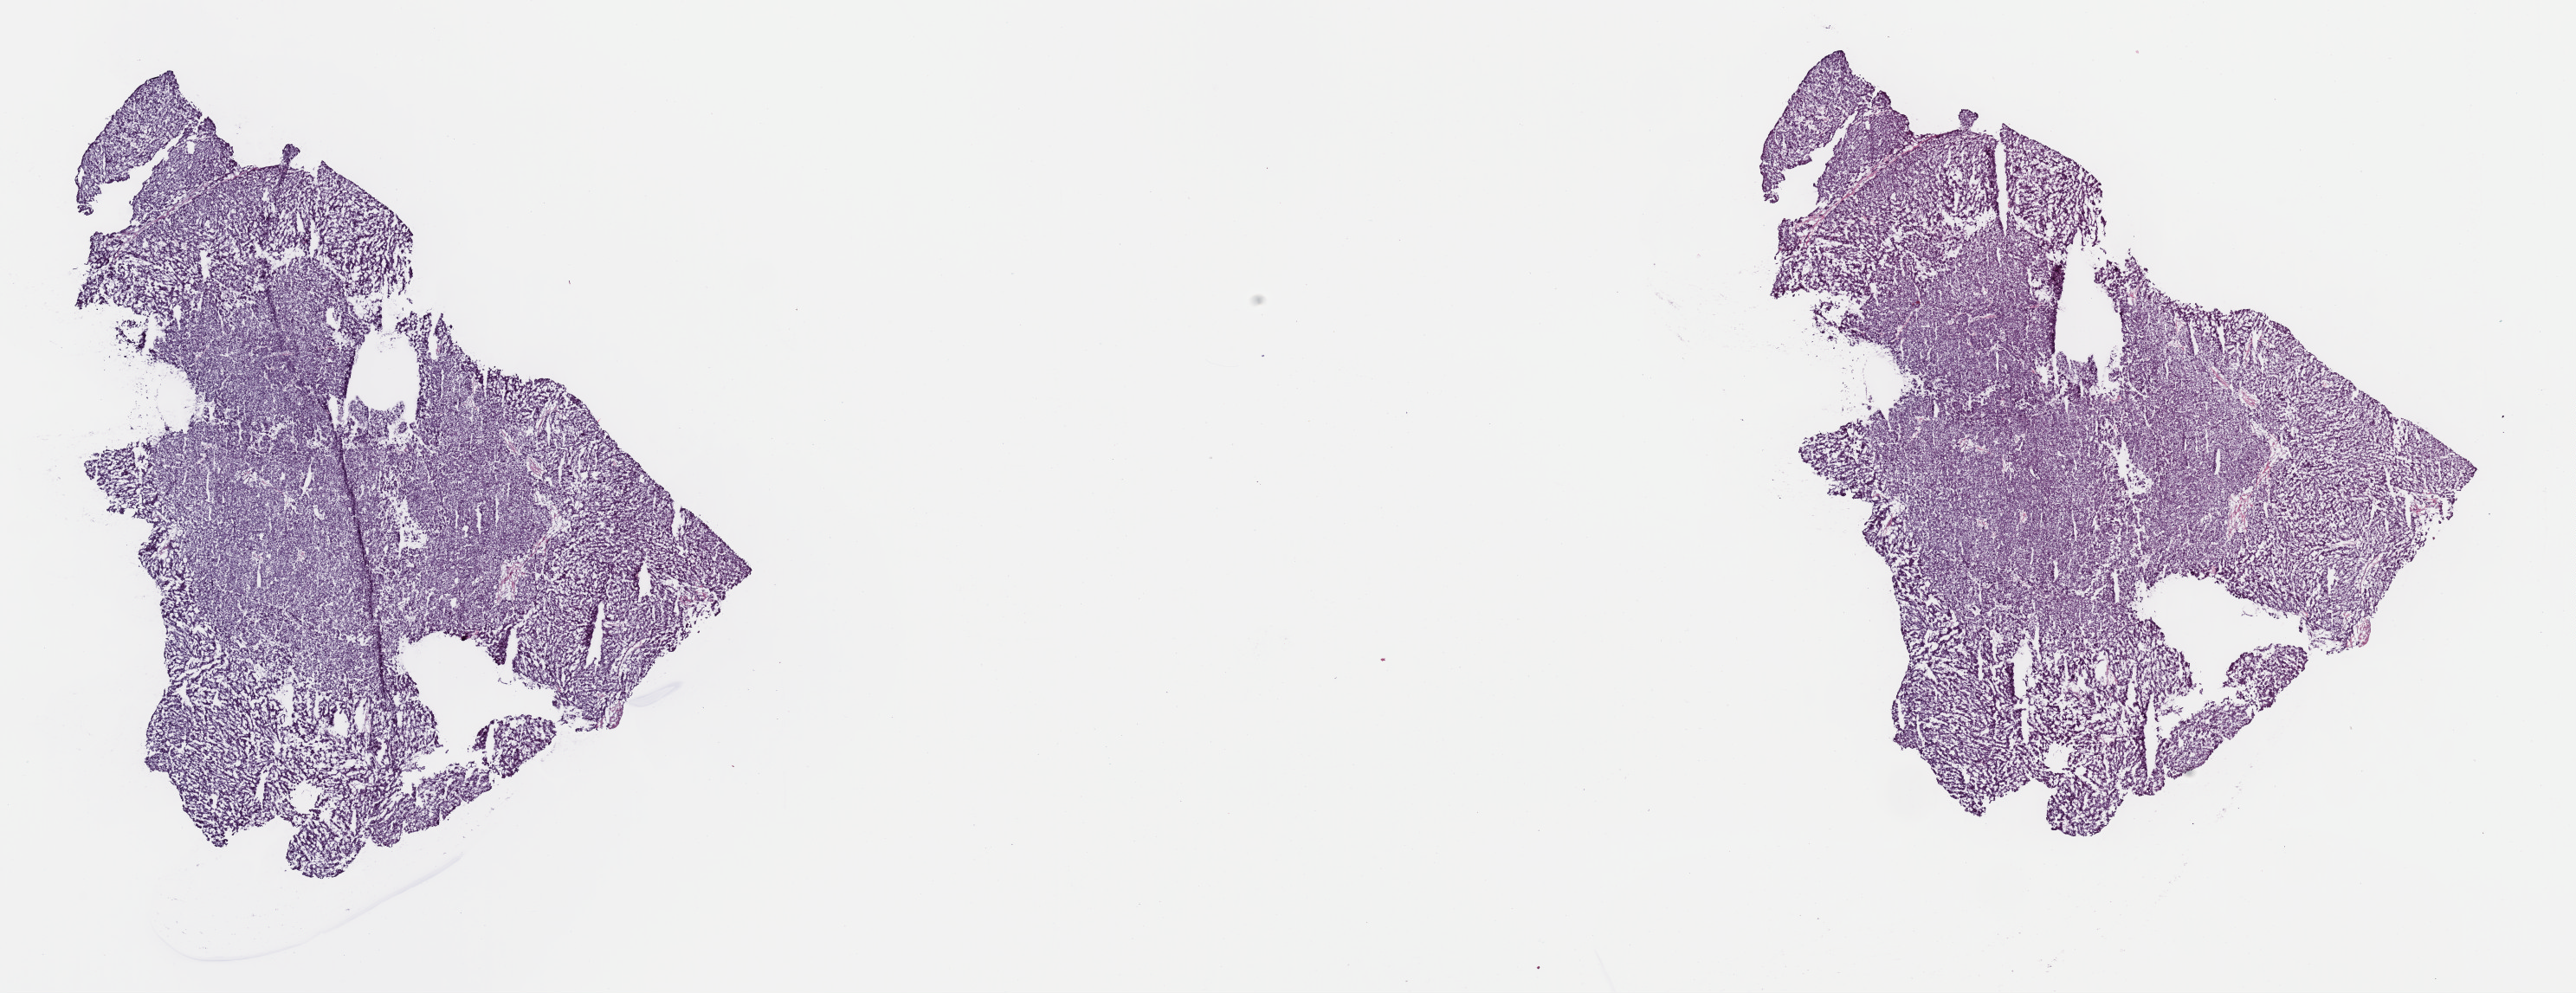
Whole-slide histology image, H&E-stained, shown as a low-resolution overview of the whole scanned area (about 23.5 x 9.1 mm, slide scanned at 40x), frozen section from the top of the tissue portion, primary tumour sample from the liver. Female patient; age at initial diagnosis 66 years. Histologic grade: G2 (moderately differentiated). Pathologist review of this section (percent, as recorded): tumour cells 100%, tumour nuclei 95%, normal cells 0%, stromal cells 0%, necrosis 0%. Inflammatory infiltration, as recorded: lymphocyte infiltration 0%, monocyte infiltration 0%, neutrophil infiltration 0%.
- AJCC pathologic stage: I (7th edition)
- diagnosis: Hepatocellular carcinoma, NOS